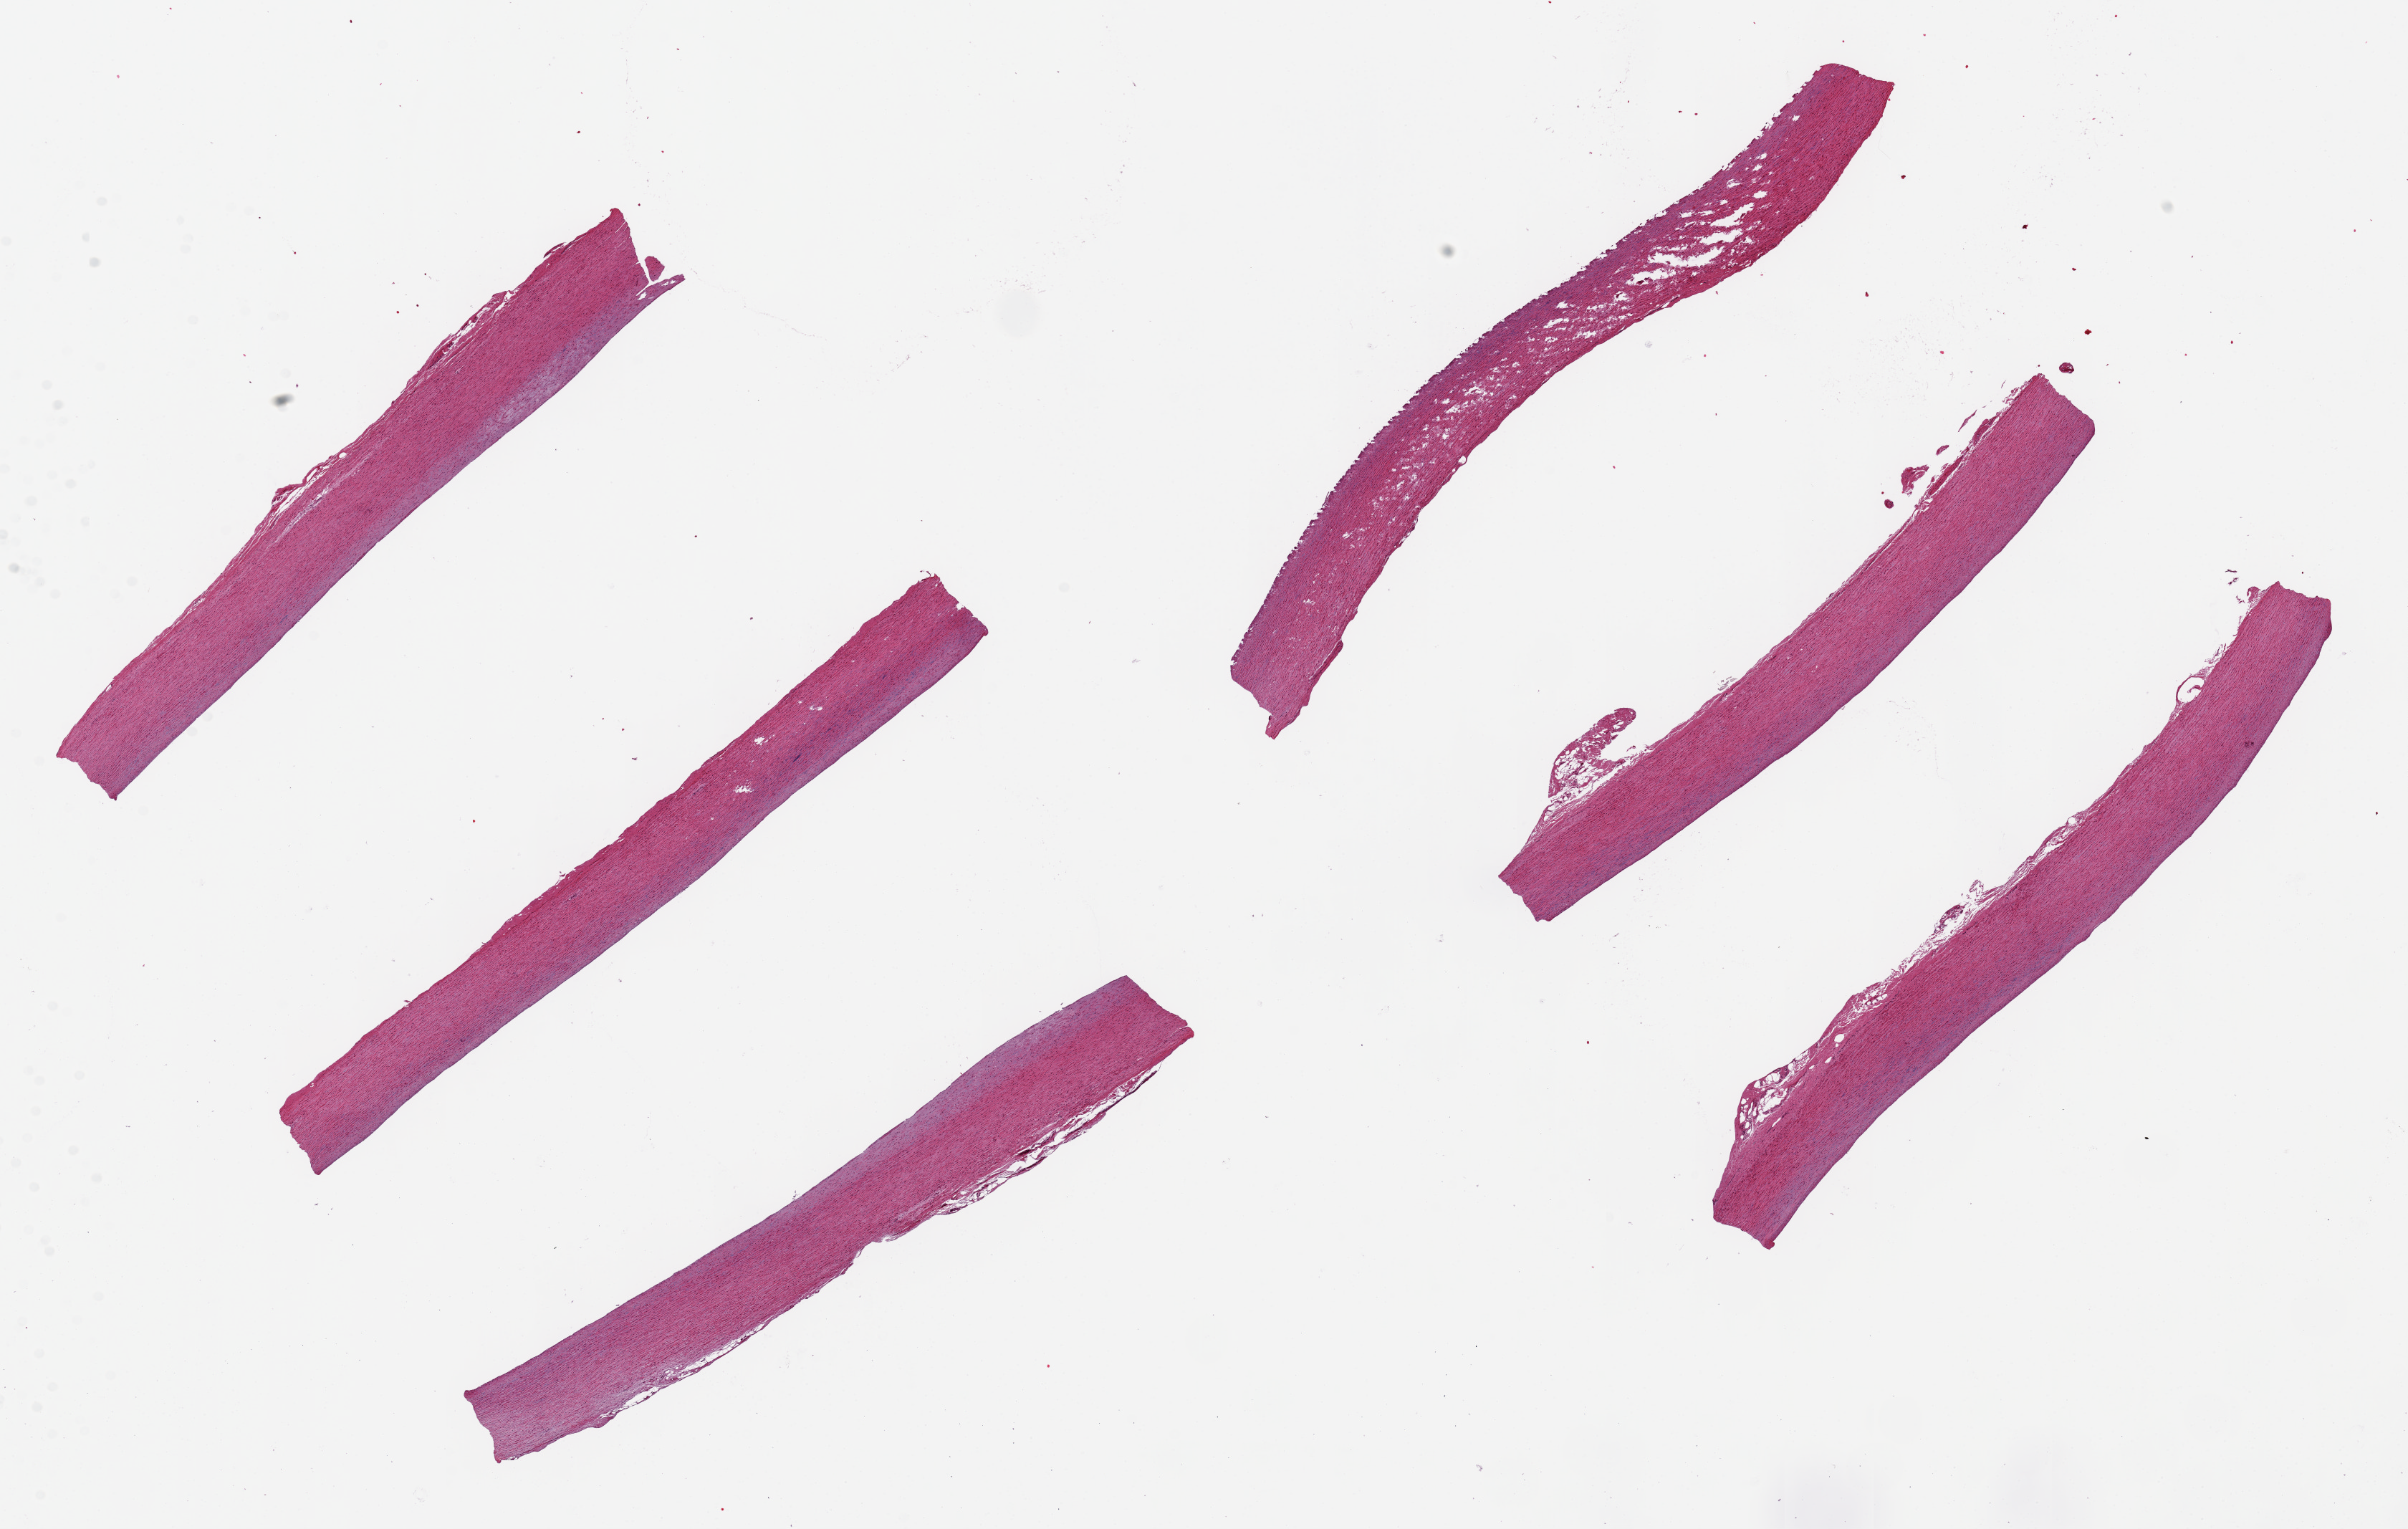
Hematoxylin and eosin (H&E) whole-slide image, shown as a low-resolution overview of the whole scanned area (about 26.6 x 16.9 mm, slide scanned at 20x). PAXgene-fixed paraffin-embedded (PFPE) section. Sampled site (target tissue): aorta. Tissue donor sample. Male donor.
Reviewer comment on this tissue sample: 6 ~9x1mm pieces. Minimal atherosclerosis.